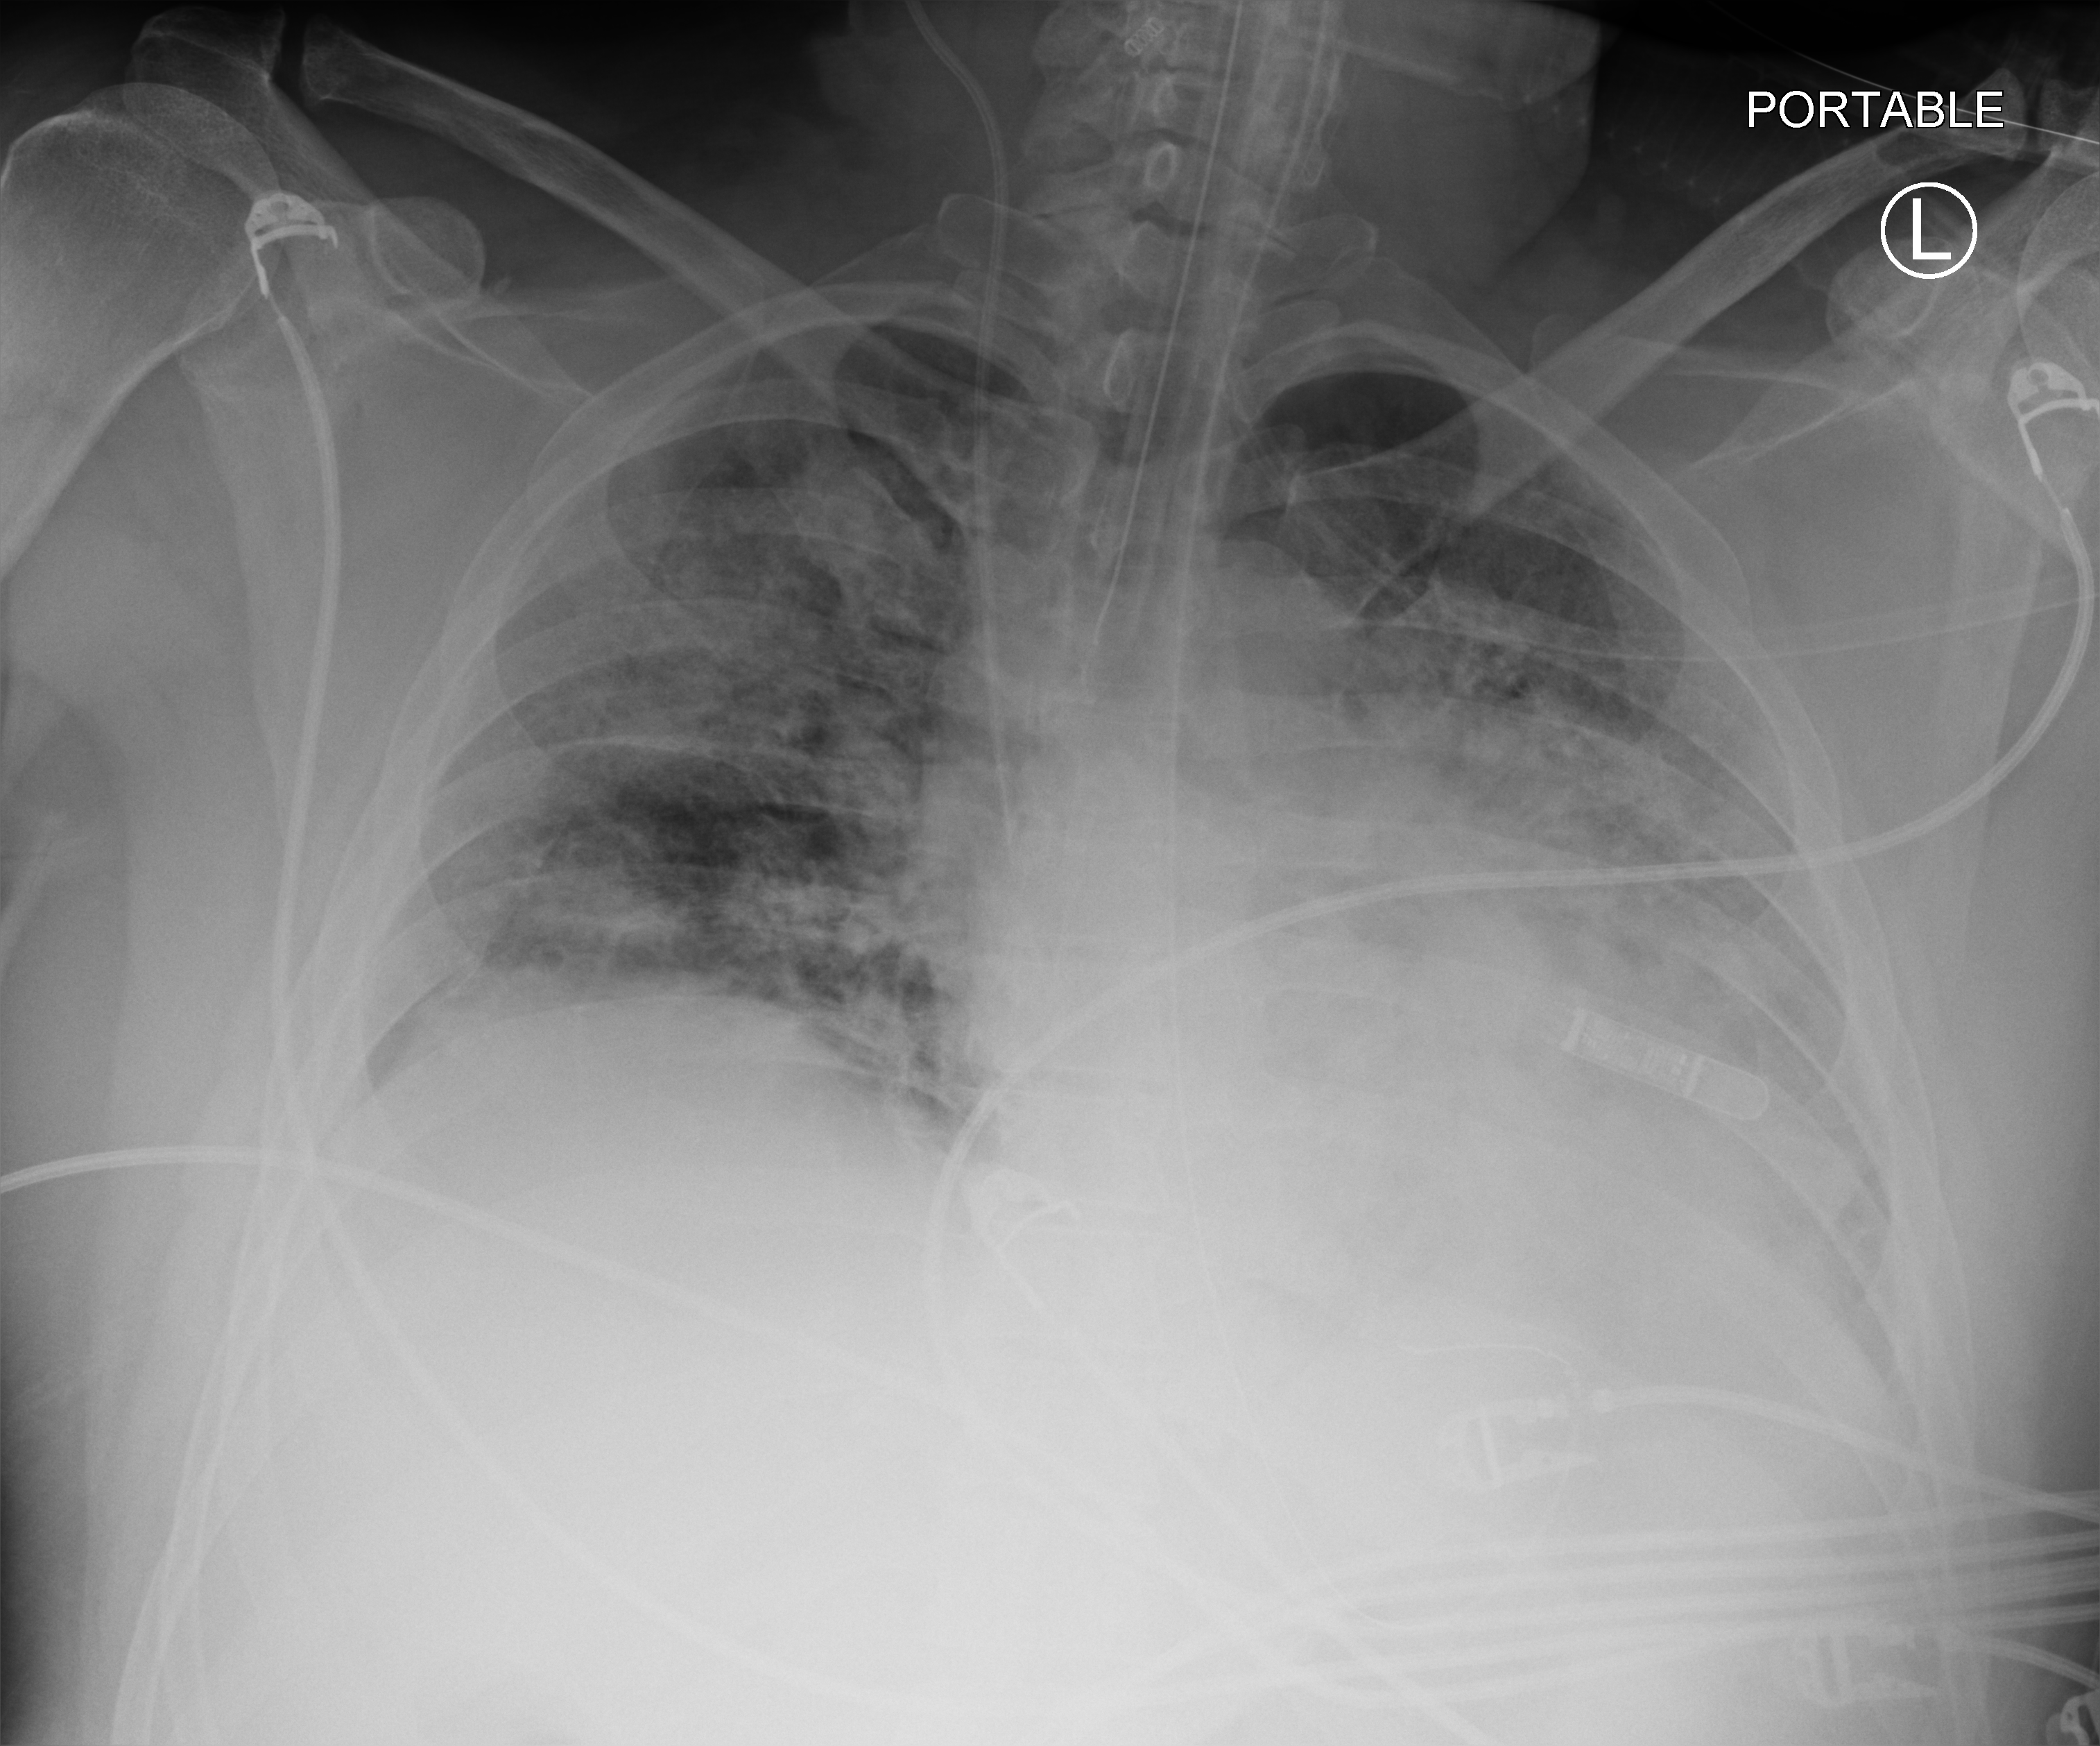
Portable chest radiograph, anteroposterior (AP) projection. Male patient hospitalised with COVID-19, age 18–59 years.
From the hospital-stay record, not from the radiograph (when in the stay this image was taken is not recorded):
- admitted to intensive care during this hospital stay: yes